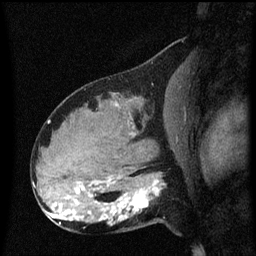
Breast MRI (dynamic contrast-enhanced), one sagittal slice. Position 31 of 60 along the scan axis. Dynamic contrast-enhanced series, image 2 of 3 at this slice position (ordered by acquisition). 1.5 T. TE 4.2 ms, TR 8.4 ms. 256 × 256 image matrix. Female patient, age 31 years. From the clinical record (not read from this slice): setting: breast cancer imaged before/during neoadjuvant chemotherapy; receptor status: HR-positive, HER2-negative.
Outlined on this slice (semi-automatically segmented with operator editing):
- analysis volume of interest (the breast-tissue region the enhancement analysis was run in; not a lesion): box from (x=102, y=166) to (x=169, y=229) px
- tumour enhancement mask (voxels above the 70 % enhancement threshold inside the analysis volume of interest): (x=112, y=180)–(x=159, y=225)